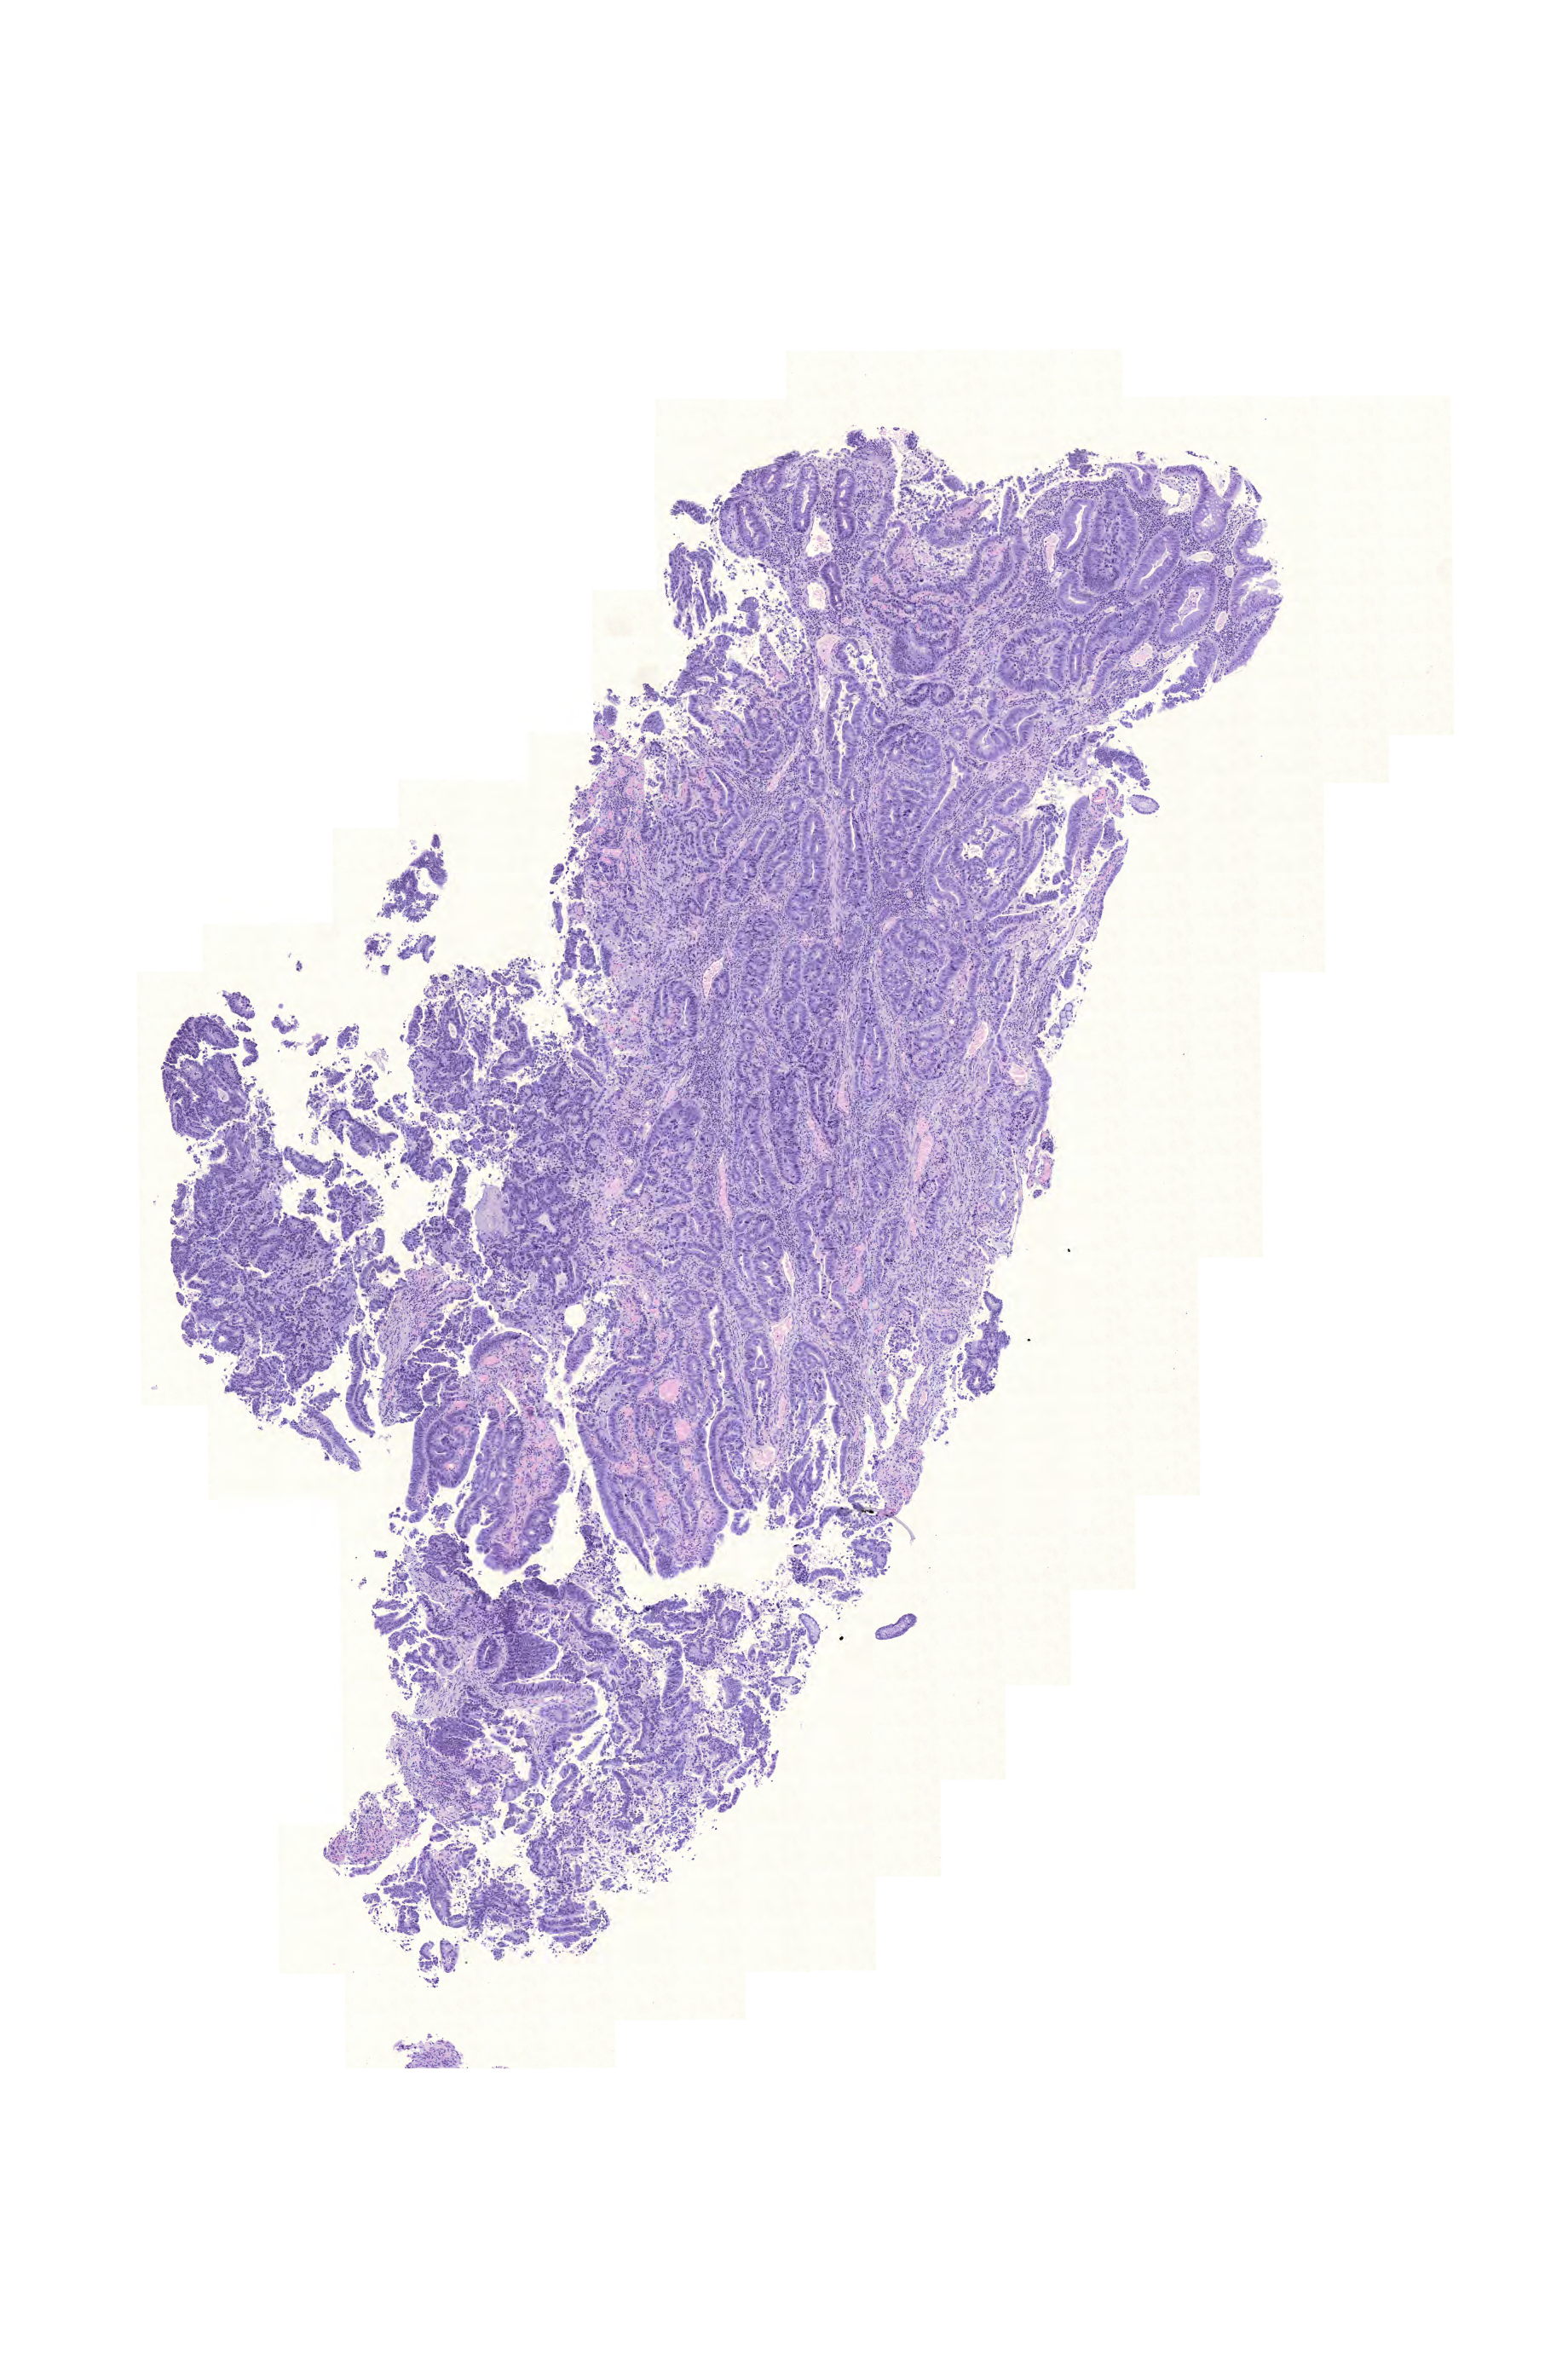
Hematoxylin and eosin (H&E) stained whole-slide image — a low-resolution overview of the entire scanned area, about 6.8 x 10.3 mm; FFPE section; primary tumour sample from the colon. Patient: female, age at initial diagnosis 74 years.
* AJCC pathologic stage: IIA (6th edition)
* lymph nodes positive (case pathology): 0 of 16 examined
* pathologic diagnosis: Adenocarcinoma, NOS (sigmoid colon)